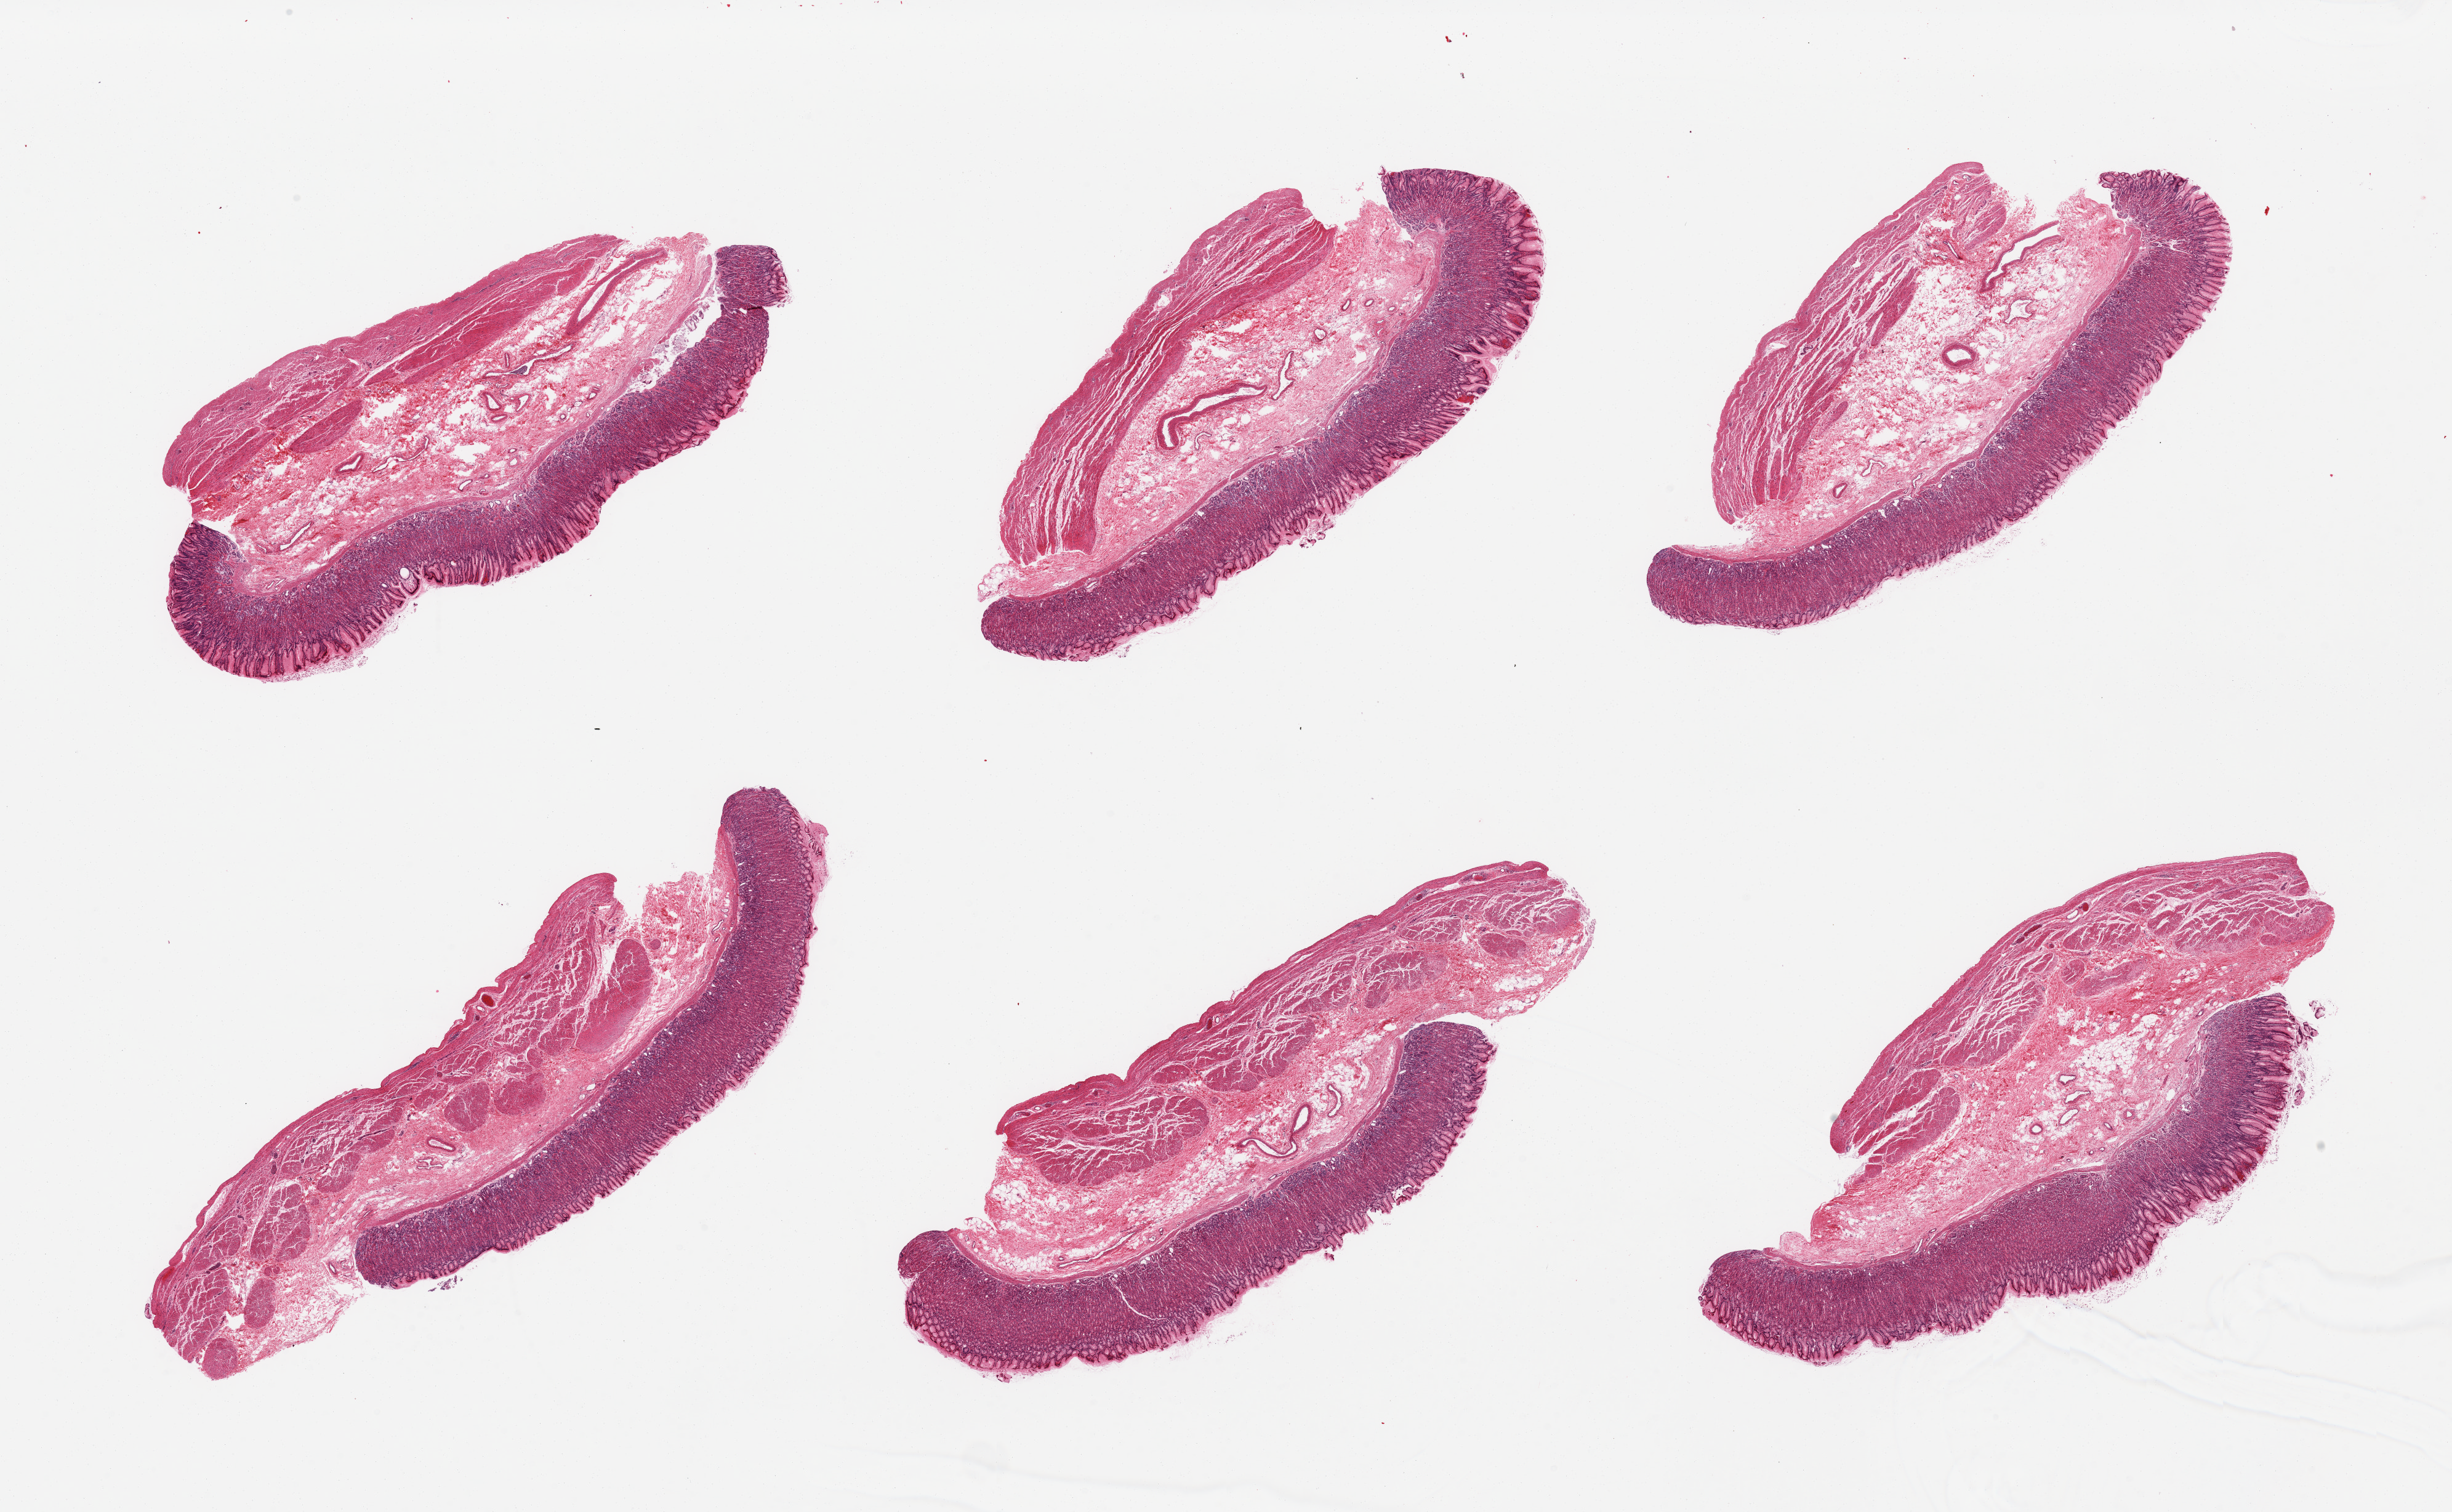
Whole-slide image, H&E stain — low-resolution overview of the scanned area, about 31.5 x 19.4 mm (slide scanned at 20x); PAXgene-fixed paraffin-embedded (PFPE) section; target tissue: stomach; donor tissue sample. Donor sex: female.
- pathologist's review note for this sample: 6 pieces, well preserved, mucosa is ~1 mm~30% thickness, no notable abnormalities